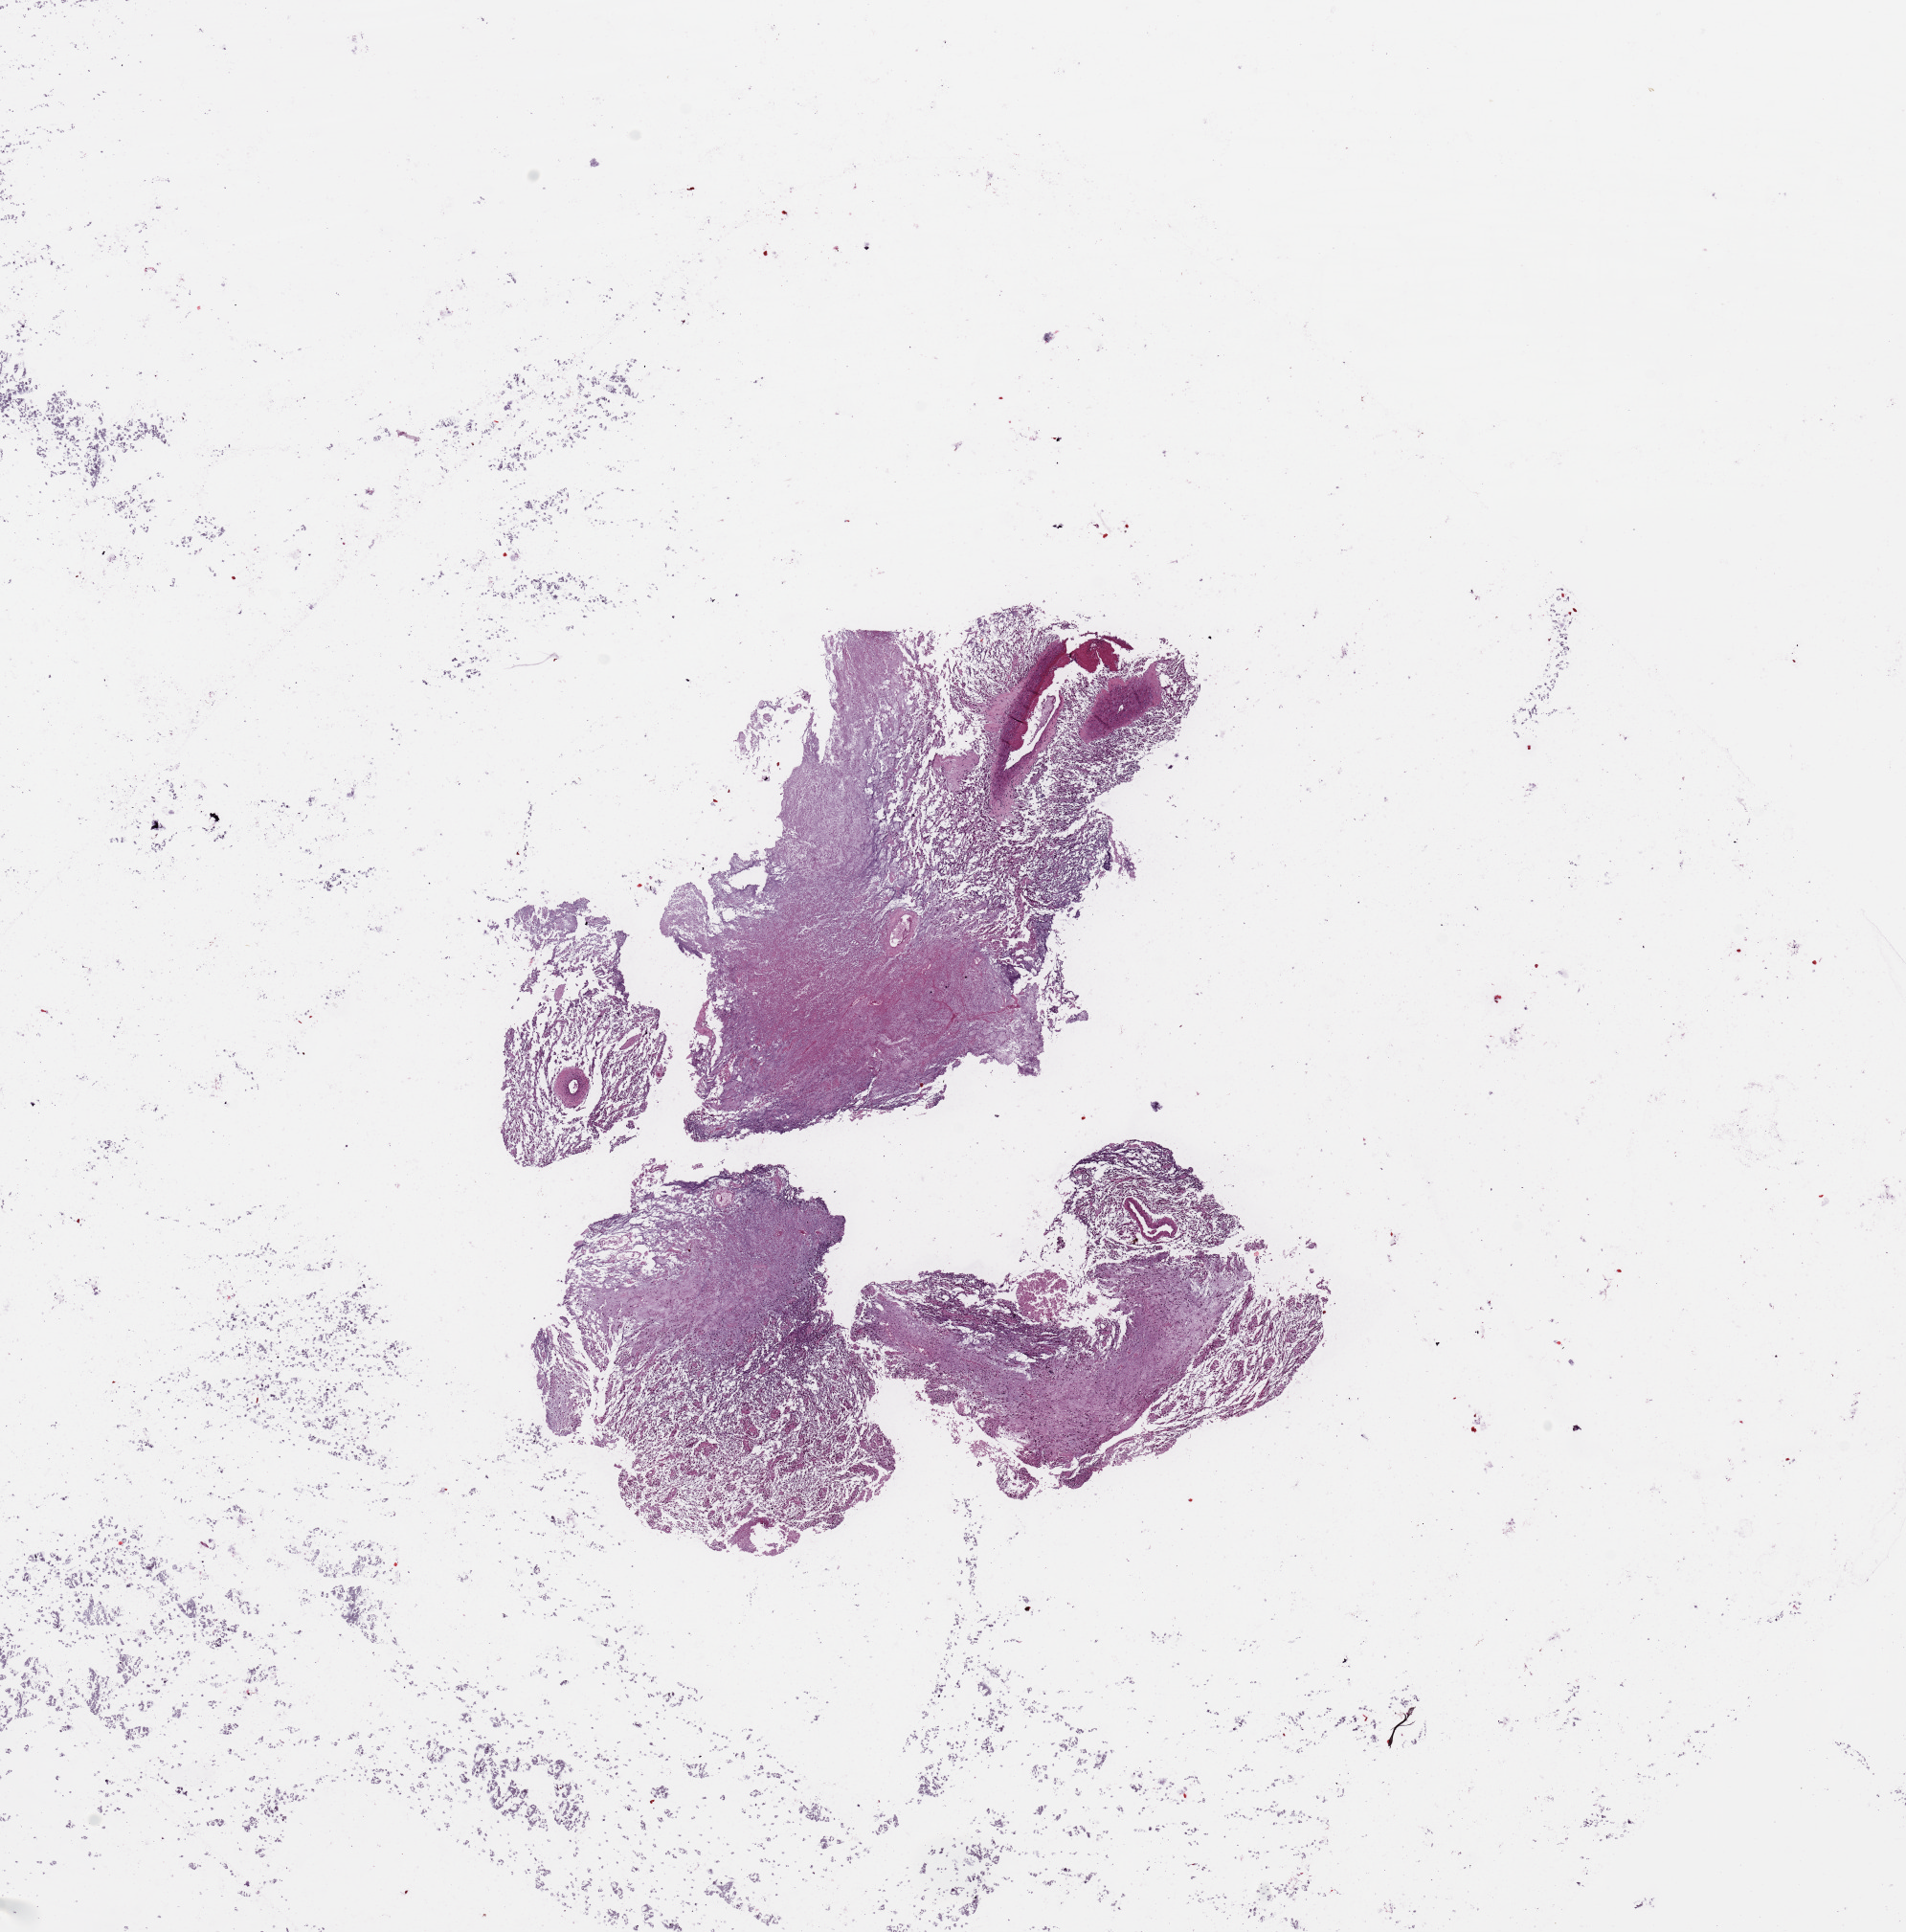
H&E-stained whole-slide image, whole scanned area (about 15.8 x 16.0 mm, acquisition: 20x scan) shown as a low-resolution overview. Brain, tumour tissue. Patient: female, age 24 years.
- diagnosis: Glioblastoma